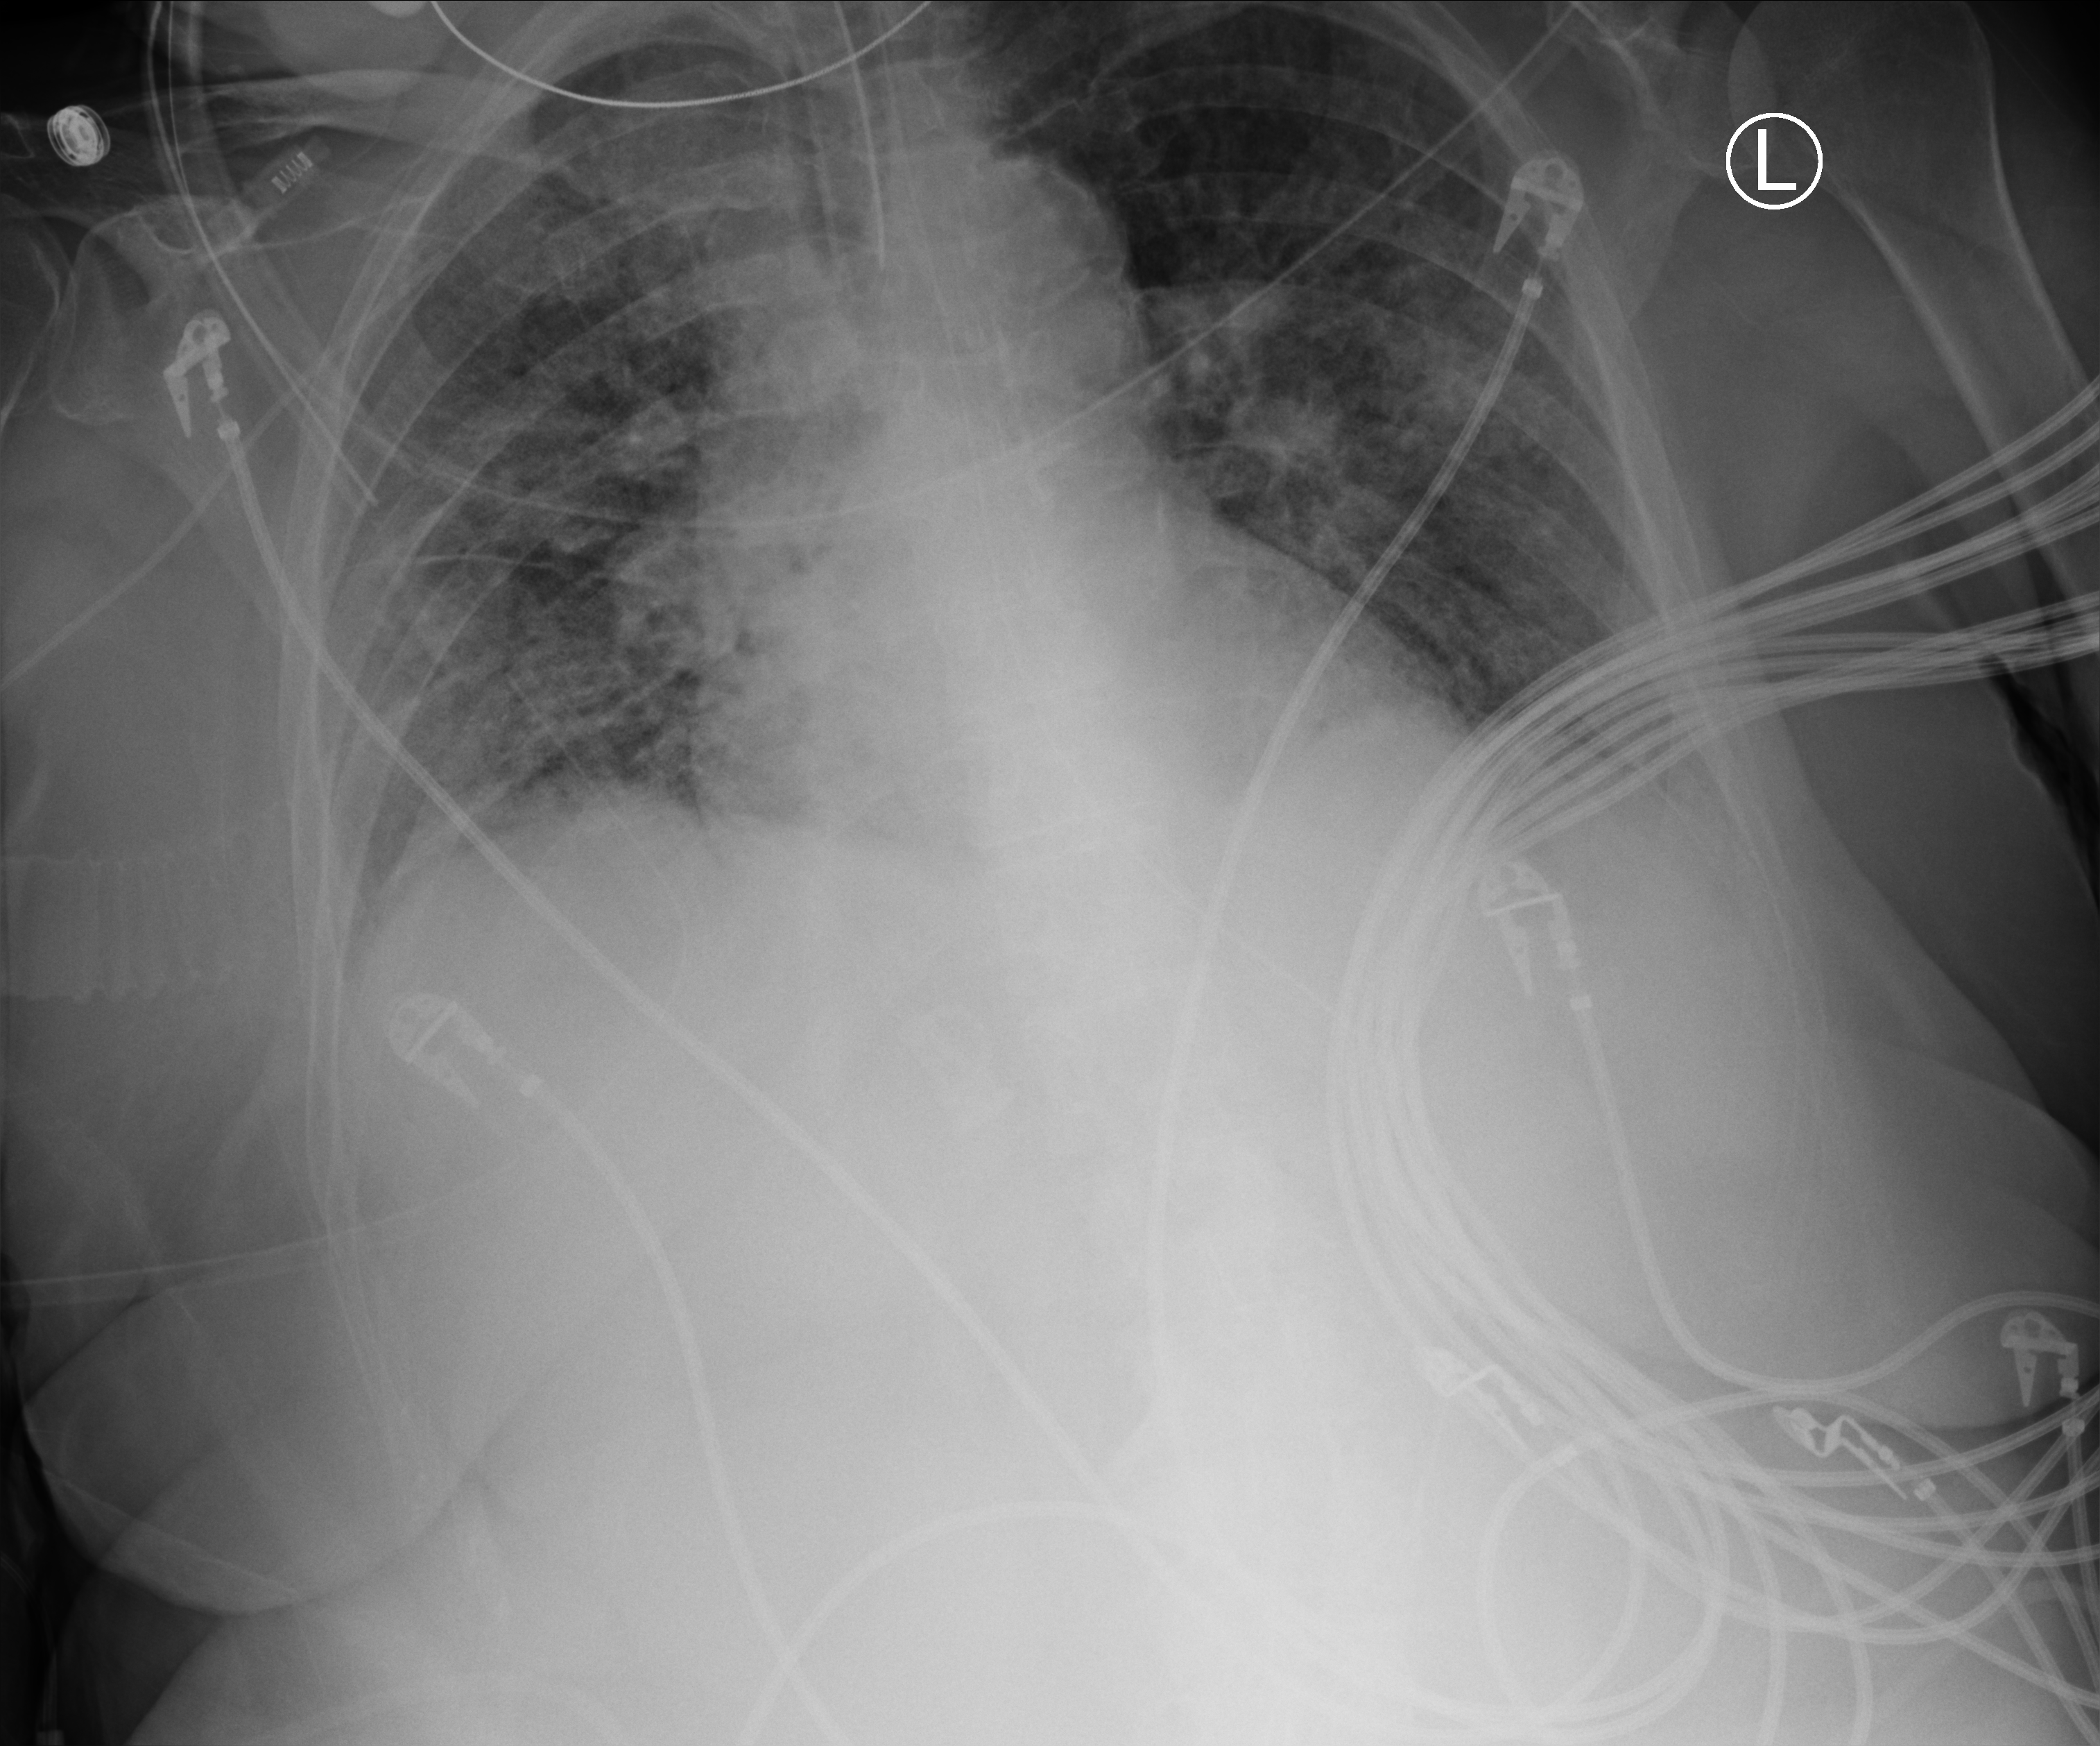
Bedside chest radiograph (computed radiography); anteroposterior (AP) projection. Patient hospitalised with COVID-19; female, aged 75–90 years.
Admission-level facts for this patient (not findings on this image; timing relative to this image not recorded):
- mechanically ventilated during this hospital stay: yes
- hypertension (admission record): yes